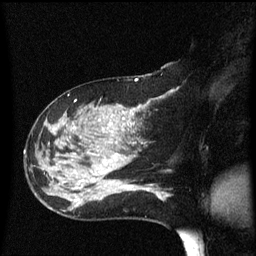
Breast MRI (dynamic contrast-enhanced), one sagittal slice; slice 27 of 60 in the series (ordered by position); dynamic contrast-enhanced series, image 2 of 3 at this slice position (ordered by acquisition); 1.5 T; TE 4.2 ms, TR 8.4 ms; 2.2 mm slice thickness; 256 × 256 image matrix, field of view 200 × 200 mm. Patient: female, 47 years.
Structures marked on this image (semi-automatic segmentation, software-assisted and operator-edited):
- analysis volume of interest (the breast-tissue region the enhancement analysis was run in; not a lesion): bounding box (x1, y1, x2, y2) in pixels: (28, 97, 149, 206)
- tumour enhancement mask (voxels above the 70 % enhancement threshold inside the analysis volume of interest): (64, 107, 141, 189)